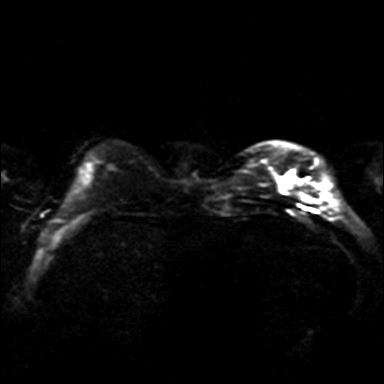
Breast MRI, one axial slice; position 7 of 36 along the scan axis; diffusion-weighted series; image 2 of 4 stored at this slice position (different b-values; order by instance number); 3 T; 4 mm slice thickness; 384 × 384 image matrix. Female patient.
Structures marked on this image (manually delineated by an expert):
- tumour on diffusion-weighted imaging: bounding box <281,170,294,192> (left, top, right, bottom; pixels)